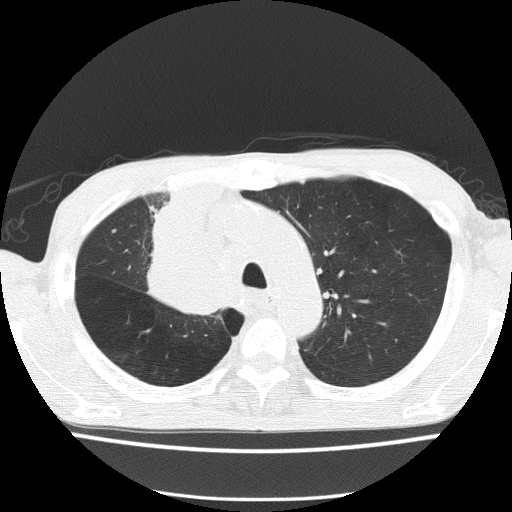
Low-dose screening chest CT, one axial slice; position 111 of 150 along the scan axis; reconstruction kernel FC51; lung window (W 1500 / L -600 HU); 512 × 512 image matrix, field of view 336 × 336 mm.
Annotated regions visible in this slice (manually delineated by an expert):
- lesion 1 (tumor, hilum of right lung): bounding box <149,189,219,315> (left, top, right, bottom; pixels)